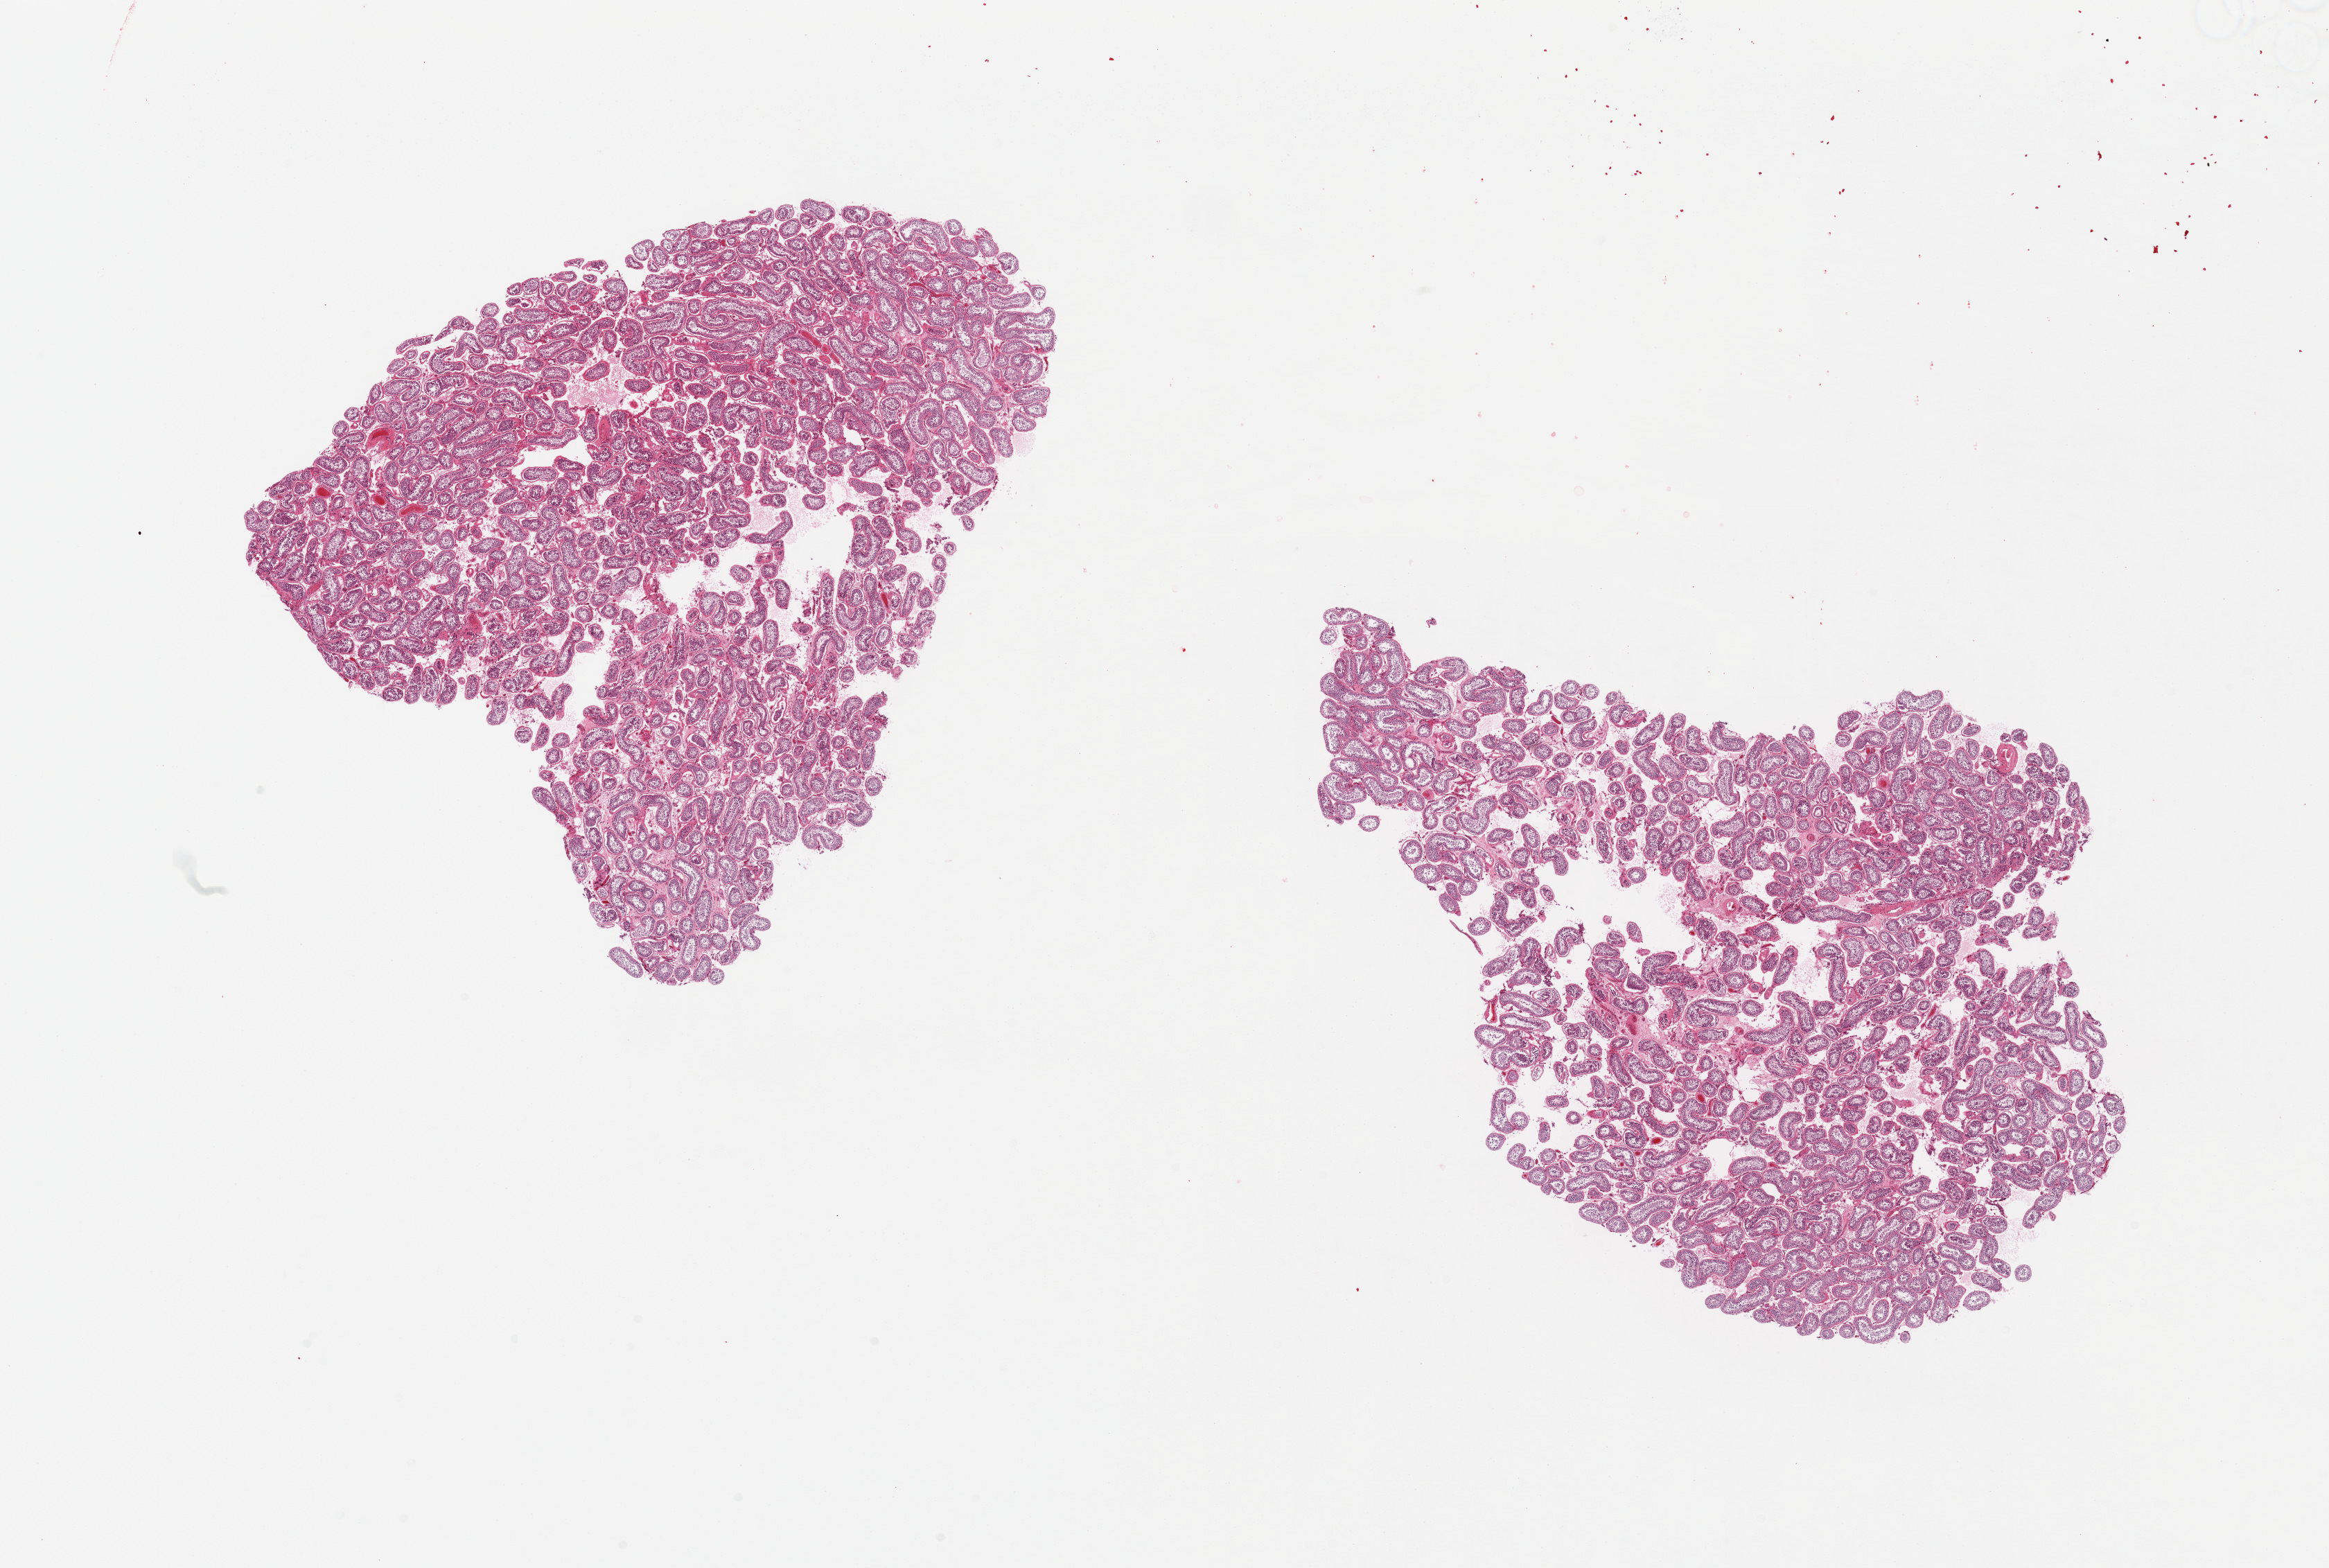
Whole-slide image, H&E stain, whole scanned area (about 26.6 x 17.9 mm) shown as a low-resolution overview. PAXgene-fixed paraffin-embedded (PFPE) section. Target tissue: testis. Tissue donor sample. Donor sex: male.
* pathologist's review note for this sample: 2 pieces. Spermatogenesis